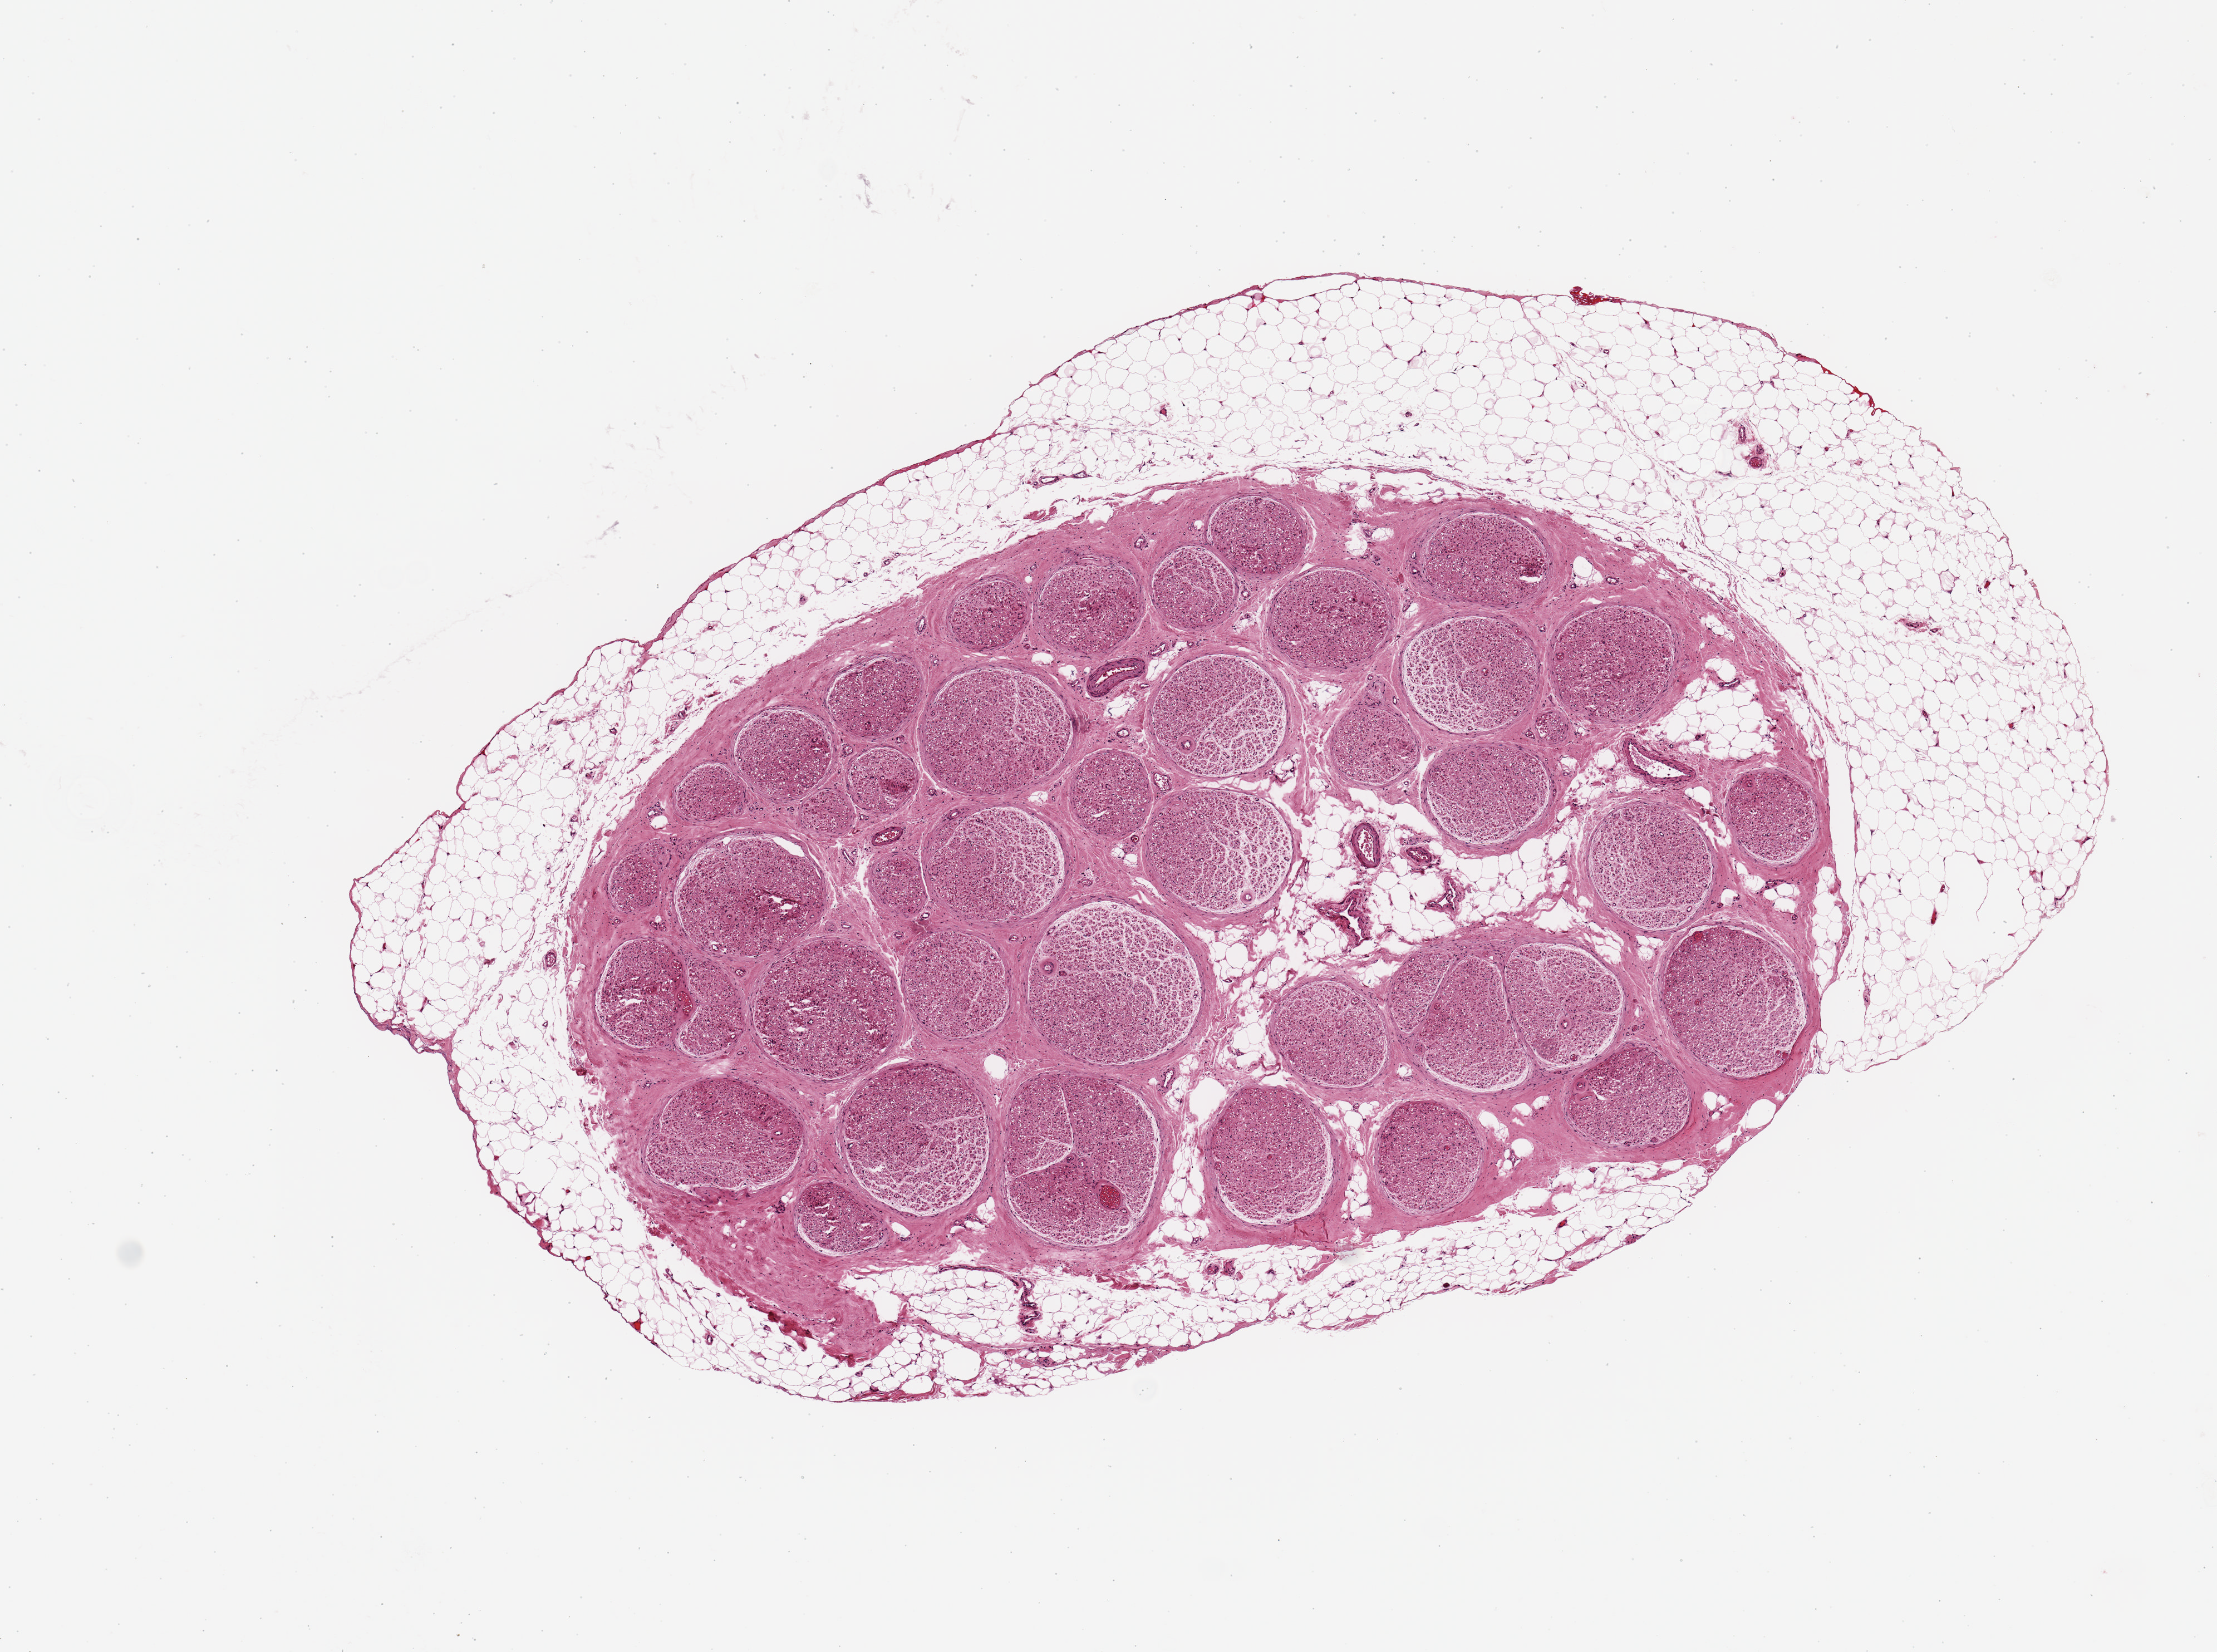
Whole-slide image, haematoxylin and eosin stain, brightfield — shown as a low-resolution overview of the whole scanned area (about 7.9 x 5.9 mm, acquisition: 20x scan), PAXgene-fixed, paraffin-embedded tissue, sampled site (target tissue): tibial nerve, tissue donor sample. Female donor.
- pathologist's review note for this sample: 4.5x2.7mm nerve with surrounding rim of fat .2-.8mm in thickness